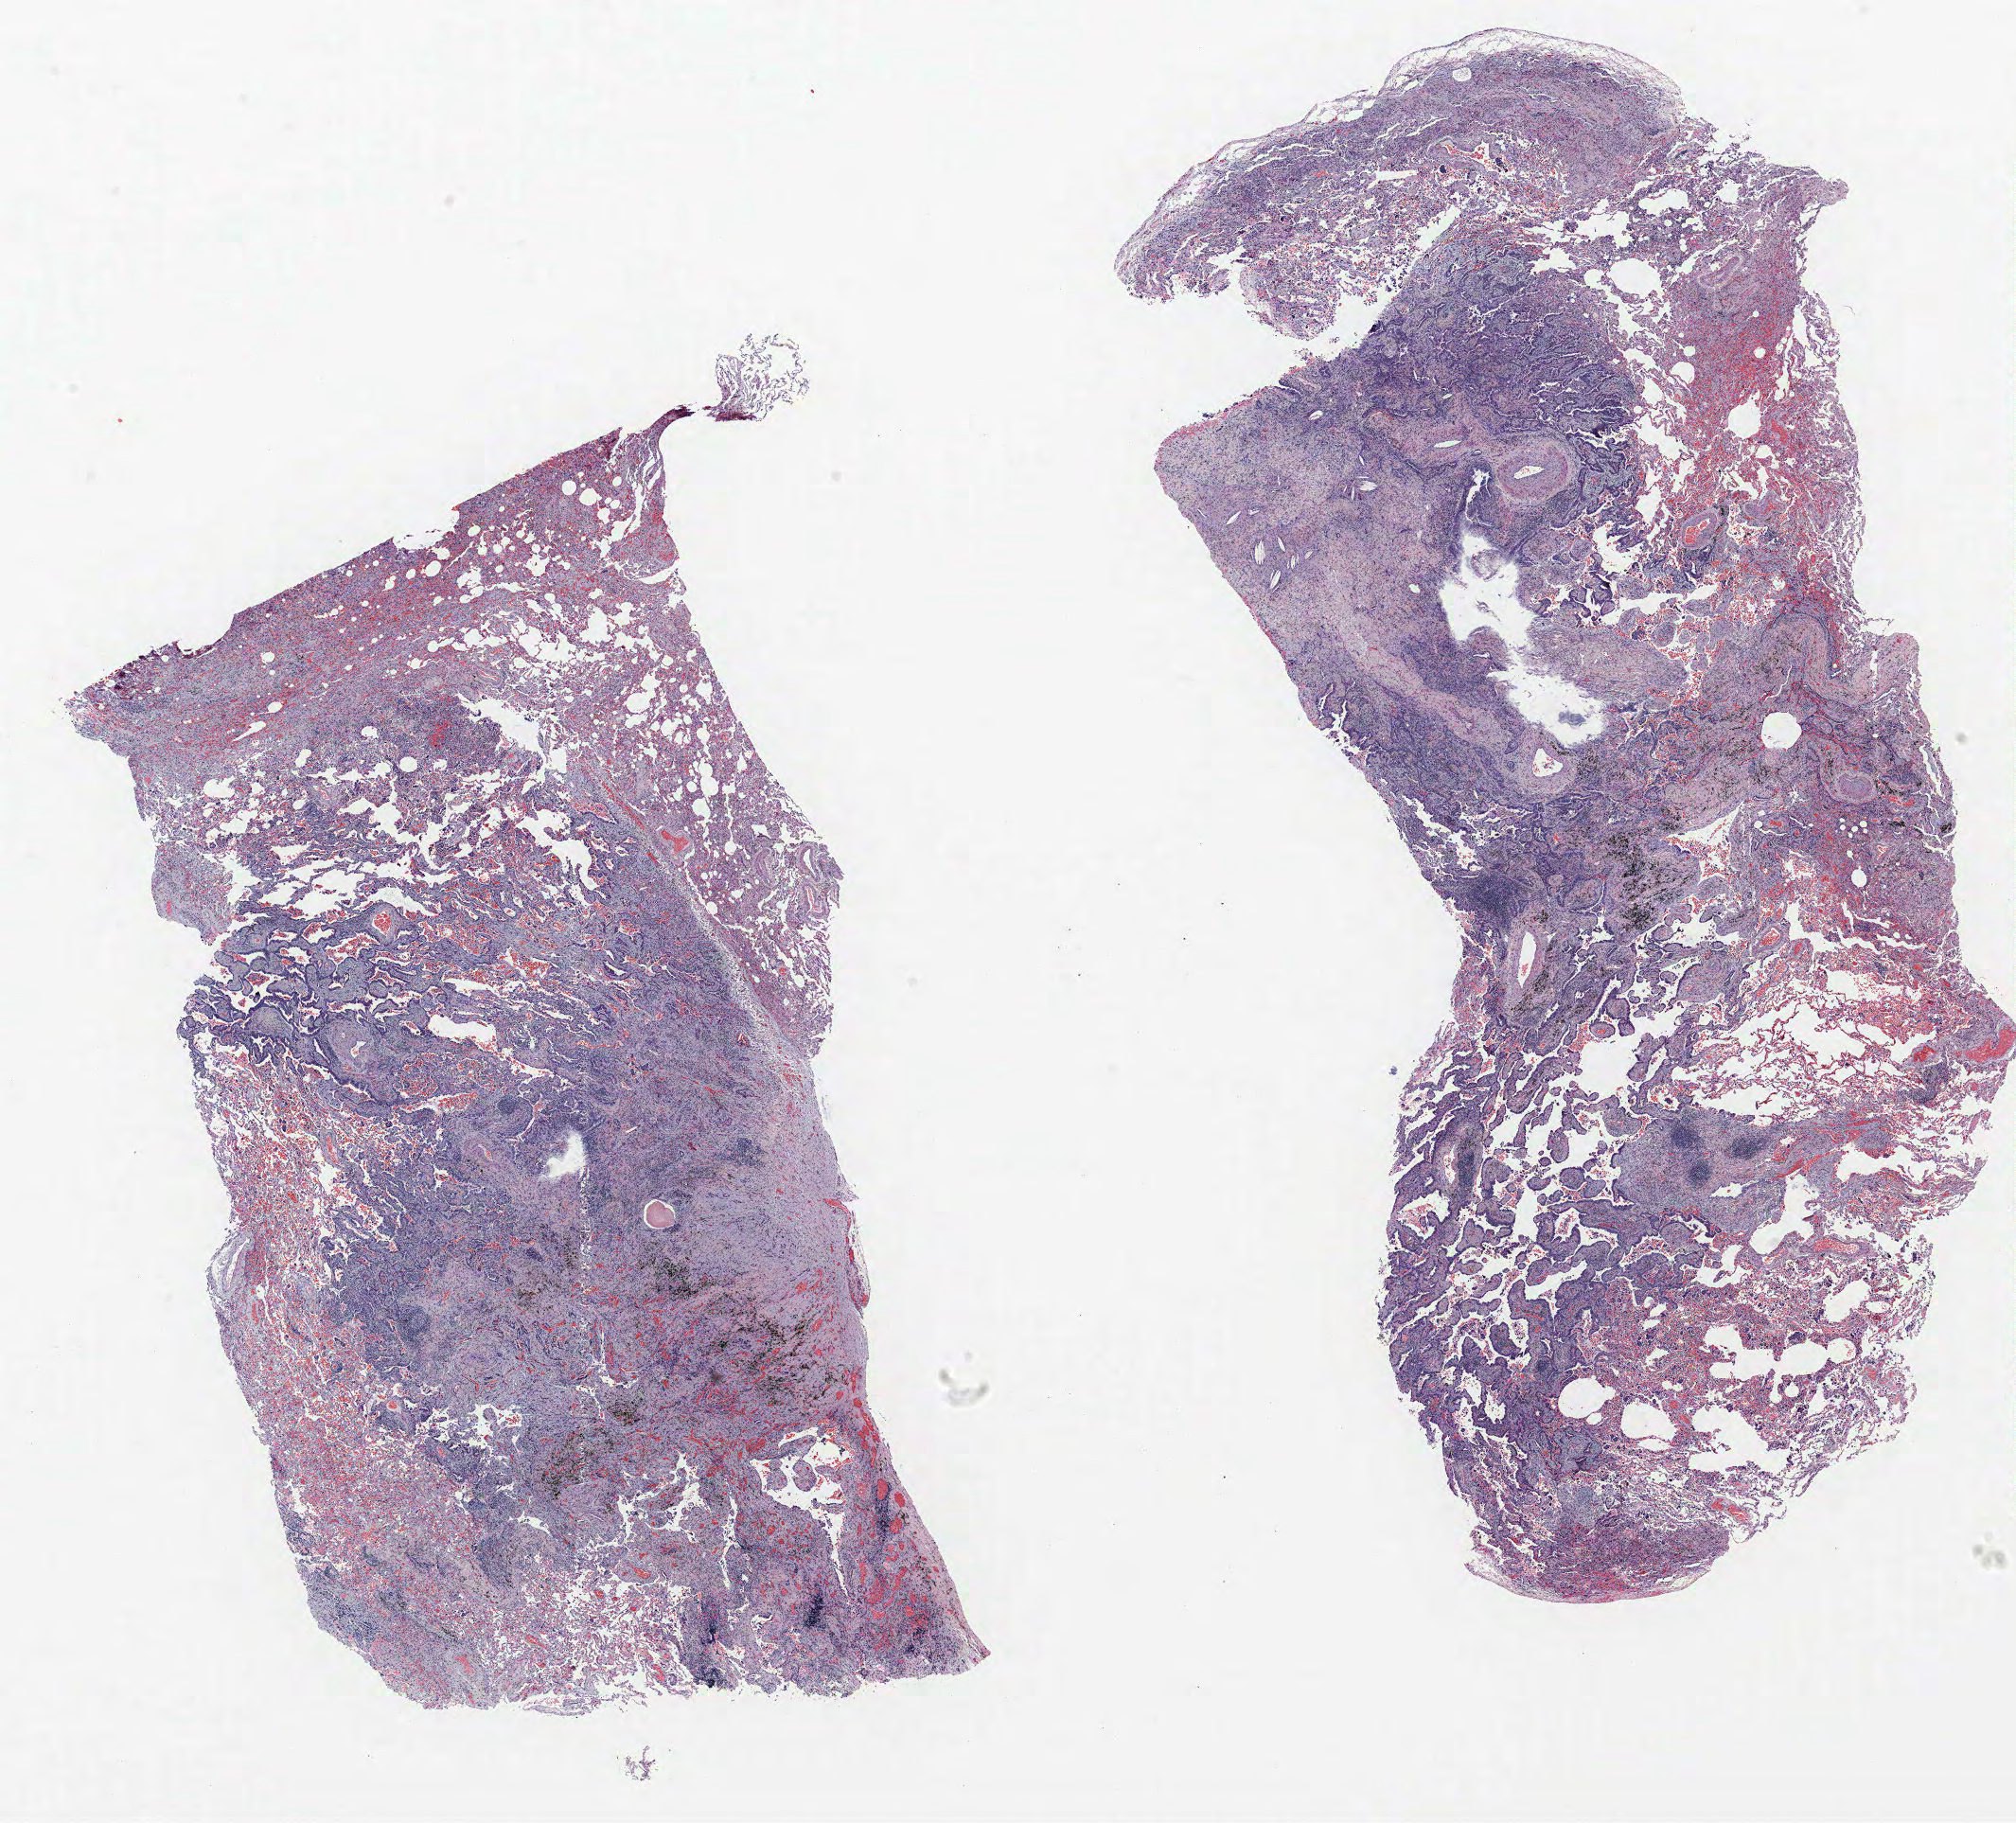
H&E-stained whole-slide image — shown as a low-resolution overview of the whole scanned area (about 17.0 x 15.4 mm, from a 40x scan), formalin-fixed paraffin-embedded (FFPE) section, lung tissue. Male, age 56 at enrolment.
Participant's lung-cancer diagnosis: Adenocarcinoma, NOS.